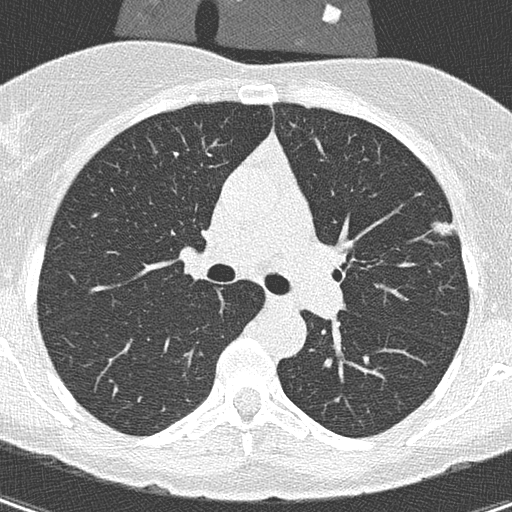
Chest CT (low-dose screening protocol), one axial image; first (baseline) screen; lung window (W 1500 / L -600 HU); 2 mm slice thickness; slice 109 of 305 in the series. Female, age 56 years at enrolment. Former smoker at enrolment.
Lesion marked by an expert reader, bounding box (x1, y1, x2, y2) in pixels: (421, 192, 469, 245). Screening reader's record for this exam (one nodule recorded; not confirmed to be the boxed lesion): non-calcified nodule or mass ≥4 mm, left upper lobe, 110 × 106 mm, spiculated (stellate) margins, soft tissue attenuation. Official screen result: positive, change unspecified: nodule(s) >= 4 mm or enlarging nodule(s), mass(es), or other non-specific abnormalities suspicious for lung cancer. Later outcome: lung cancer diagnosed 417 days after this screen (after the second annual screen) — adenocarcinoma, NOS, left upper lobe, moderately differentiated (G2), stage IA (AJCC 6th edition), 11 mm at pathology.